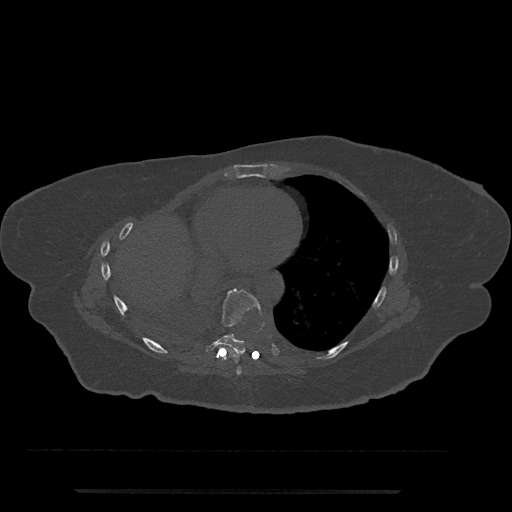
CT including the spine, one axial slice. Slice 387 of 797 in the series (ordered by position). 120 kVp. Bone window (W 1800 / L 400 HU). 0.5 mm slice thickness. 512 × 512 image matrix, field of view 440 × 440 mm. Patient: female, 51 years. Case-level facts recorded for this patient, not image findings: primary cancer: neuro; vertebrae with lytic lesions (as recorded): T8.
Annotated regions visible in this slice (semi-automatically segmented with operator editing):
- T7 vertebra: bounding box <236,366,242,375> (left, top, right, bottom; pixels)
- T8 vertebra: <205,288,264,355>
- T9 vertebra: <228,334,234,337>